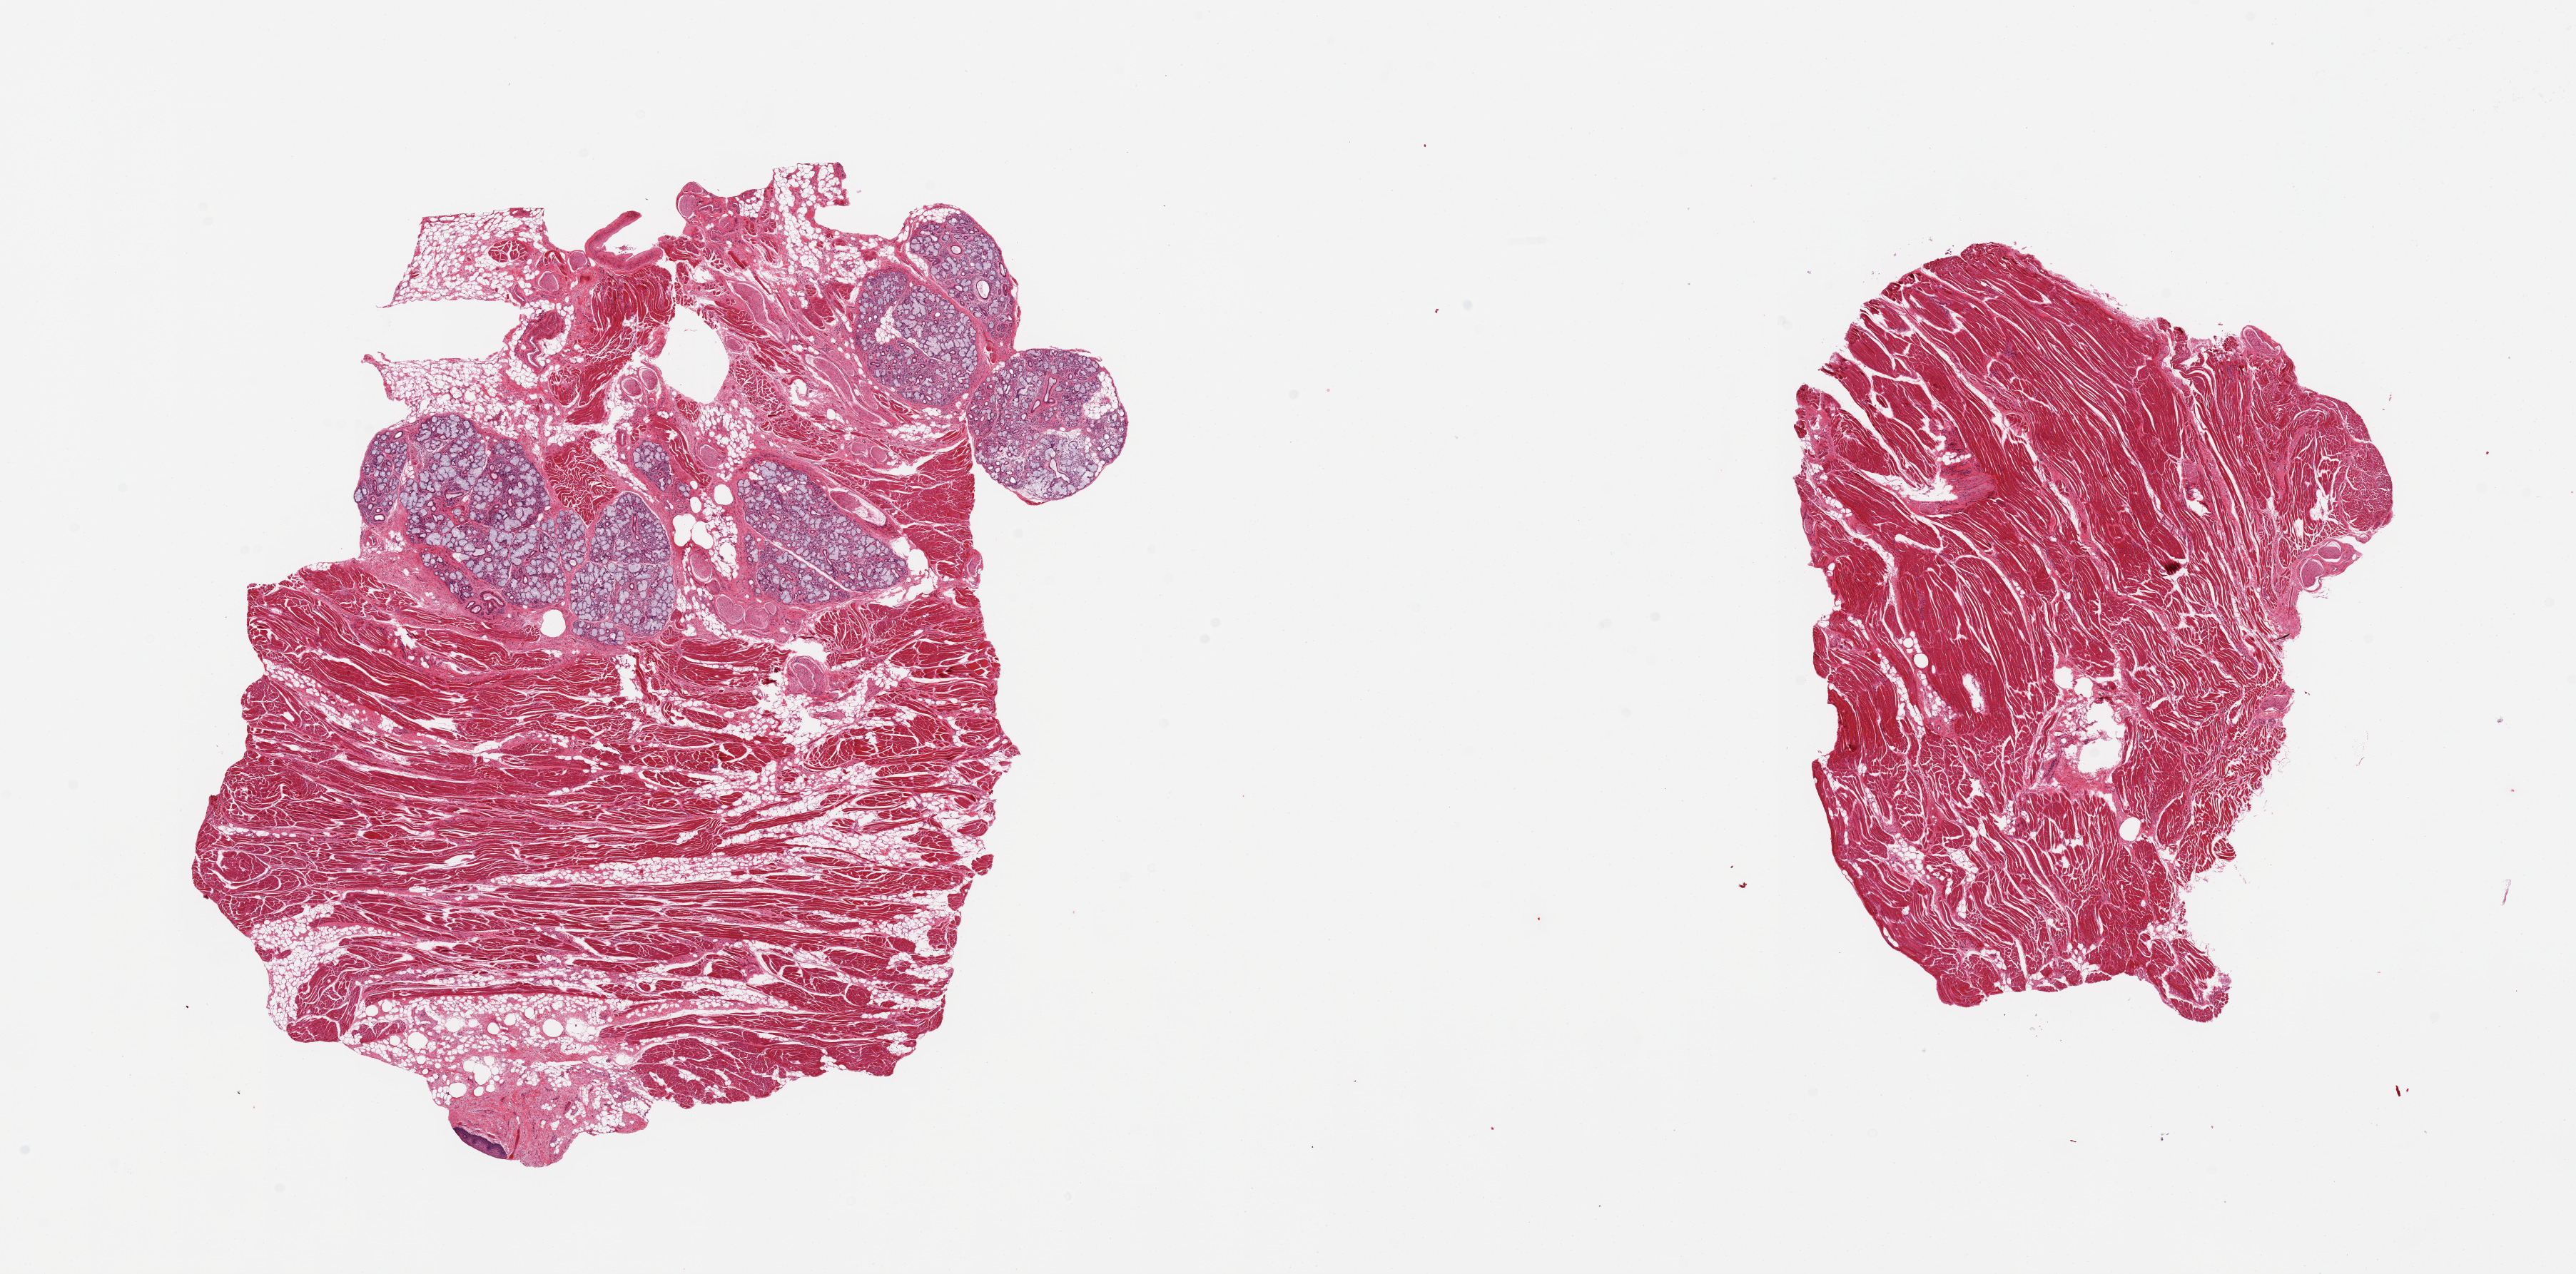
Digitized H&E-stained section — low-resolution overview of the scanned area, about 28.5 x 14.1 mm, PAXgene-fixed, paraffin-embedded tissue, target tissue: minor salivary gland, tissue donor sample. Donor sex: male.
Reviewer comment on this tissue sample: 2 pieces, ~10-15% mucinous glands, all in one section; rest is skeletal/adipose tissue.